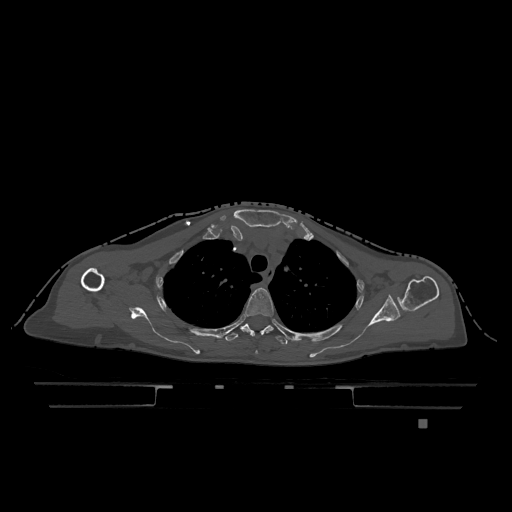
CT including the spine, one axial slice; slice 907 of 1317 in the series (ordered by position); bone window (W 1800 / L 400 HU); 0.5 mm slice thickness; 512 × 512 image matrix, field of view 500 × 500 mm. Patient: female, 74 years. Case-level facts recorded for this patient, not image findings: primary cancer: lung; vertebrae with lytic lesions (as recorded): T1, T4, T5, T6, L4, L5.
Outlined on this slice (semi-automatic segmentation, software-assisted and operator-edited):
- T3 vertebra: bounding box <244,288,274,354> (left, top, right, bottom; pixels)
- T4 vertebra: <225,323,307,345>